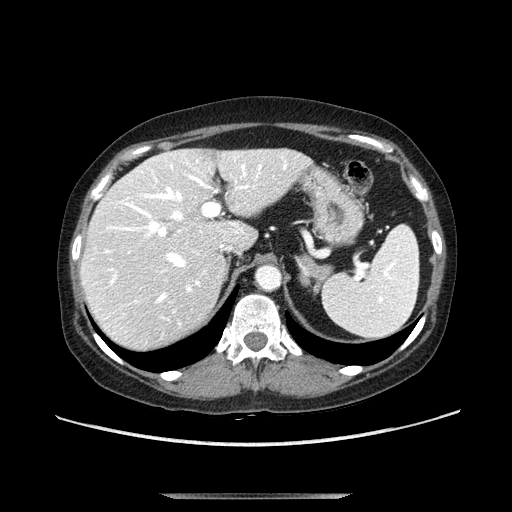
Contrast-enhanced abdominal CT, one axial slice; slice 76 of 107 in the series (ordered by position); soft-tissue window (W 400 / L 40 HU); 2.5 mm slice thickness; 512 × 512 image matrix, field of view 380 × 380 mm. Female patient. Case-level facts recorded for this patient, not image findings: diagnosis: adrenocortical carcinoma; tumour side: left adrenal; tumour size at pathology: 7.5 cm; Ki-67 index: 9 %; stage (as recorded): 3.
Structures marked on this image (semi-automatically segmented with operator editing):
- mass: box from (x=299, y=255) to (x=333, y=287) px